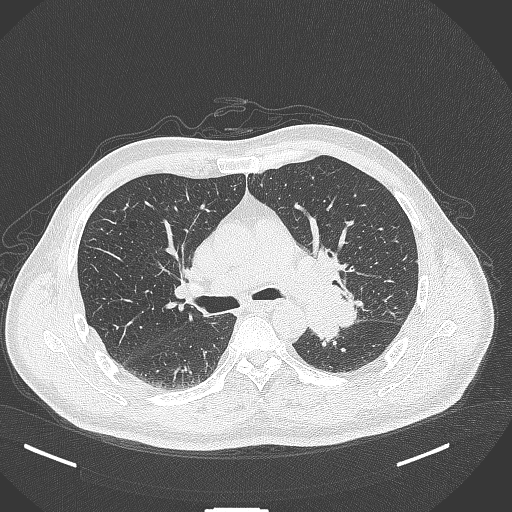
Chest CT, one axial slice; position 257 of 429 along the scan axis; reconstruction kernel B70f; lung window (W 1500 / L -600 HU); 1 mm slice thickness; 512 × 512 image matrix, field of view 400 × 400 mm. Patient: male, 55 years. From the clinical record (not read from this slice): clinical TNM (as recorded): T3 N0 M1c; histopathological grade: G3.
Annotated regions visible in this slice (rectangle marked by the reading radiologist):
- lung tumour (recorded histology: adenocarcinoma): bounding box [x1, y1, x2, y2] px = [301, 287, 365, 343]